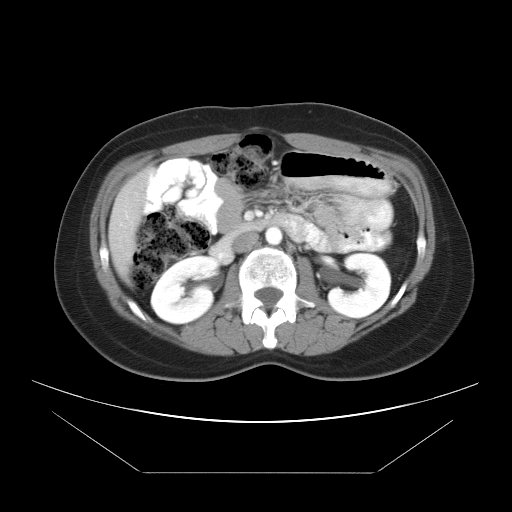
Contrast-enhanced abdominal CT, one axial slice. Position 17 of 34 along the scan axis. Intravenous contrast given. Soft-tissue window (W 400 / L 40 HU). 7.5 mm slice thickness. 512 × 512 image matrix. Female patient, age 38 years. Case-level facts recorded for this patient, not image findings: diagnosis: colorectal cancer liver metastases, imaged before liver resection; multiple liver metastases: yes; largest metastasis: 3.1 cm; disease in both lobes: no.
Structures marked on this image (manually delineated by an expert):
- liver: bounding box (x1, y1, x2, y2) in pixels: (109, 170, 152, 287)